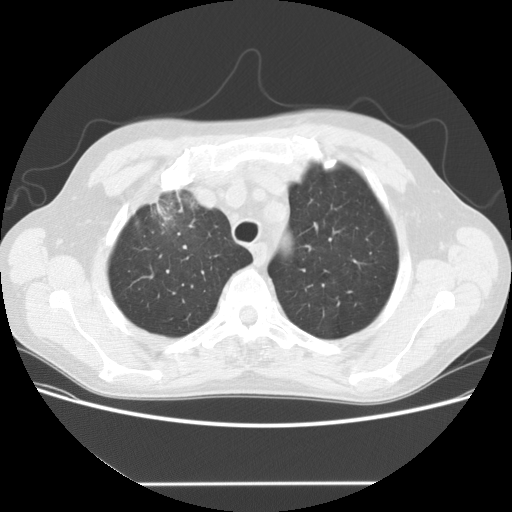
Low-dose screening chest CT, one axial slice; slice 126 of 153 in the series (ordered by position); lung window (W 1500 / L -600 HU); 512 × 512 image matrix, field of view 360 × 360 mm.
Annotated regions visible in this slice (manually delineated by an expert):
- lesion 1 (tumor, upper lobe of right lung): bounding box <155,201,173,221> (left, top, right, bottom; pixels)